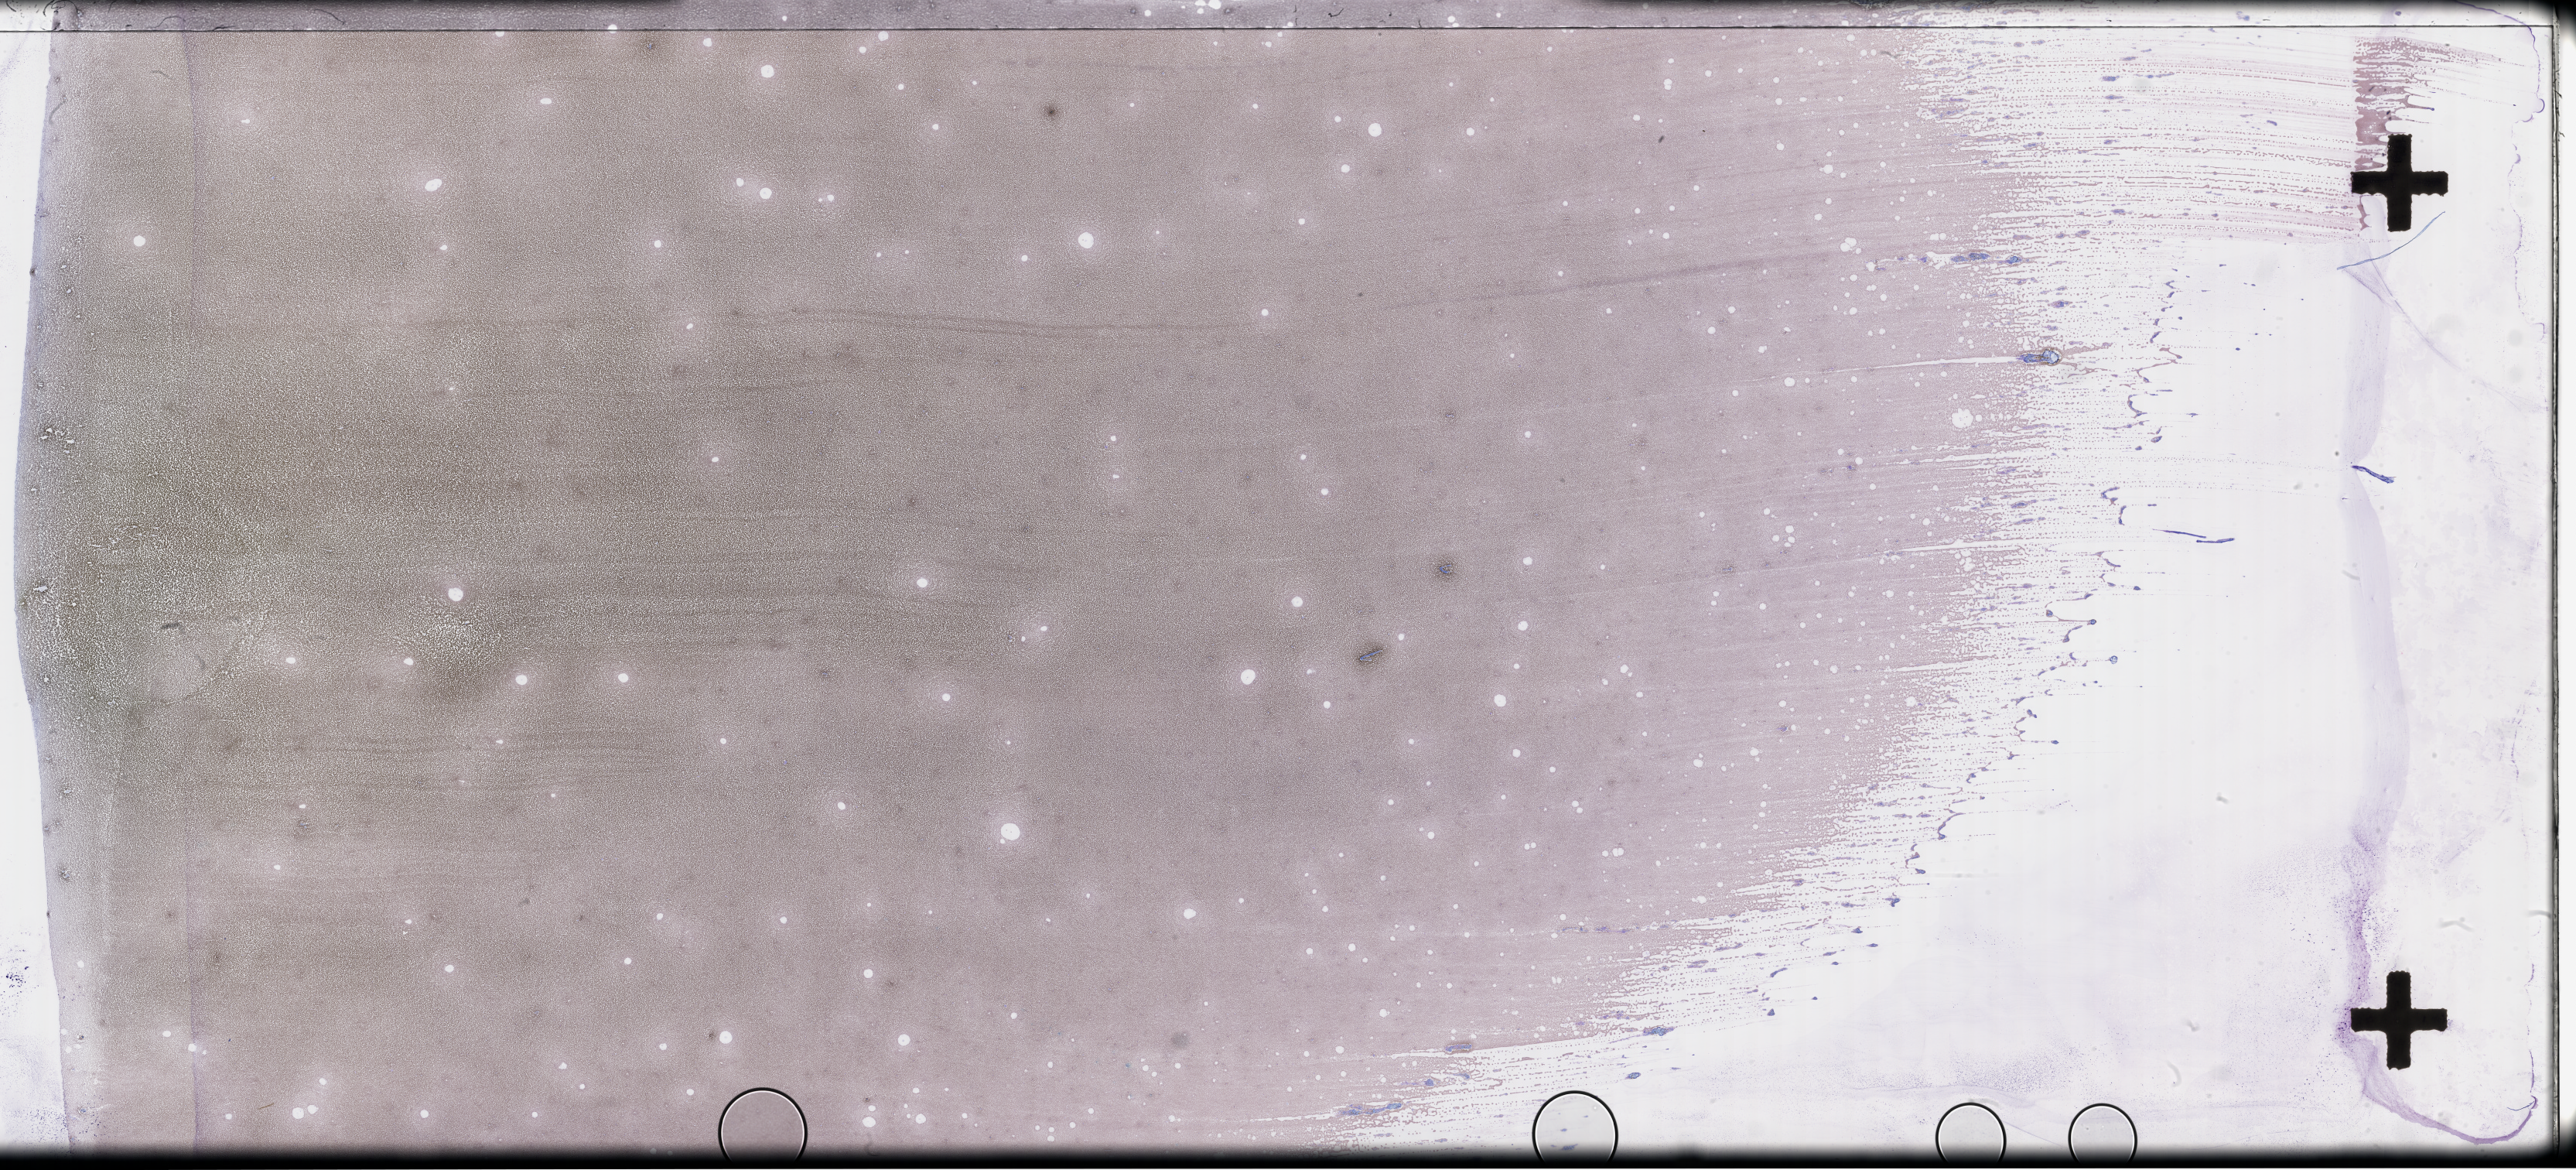
Whole-slide image of a whole blood smear, Wright-Giemsa stain — a low-resolution overview of the entire scanned area, about 53.8 x 24.4 mm. Smear from an EDTA sample. Collected on treatment. Patient sex: female.
From a patient with: Plasma Cell Myeloma.